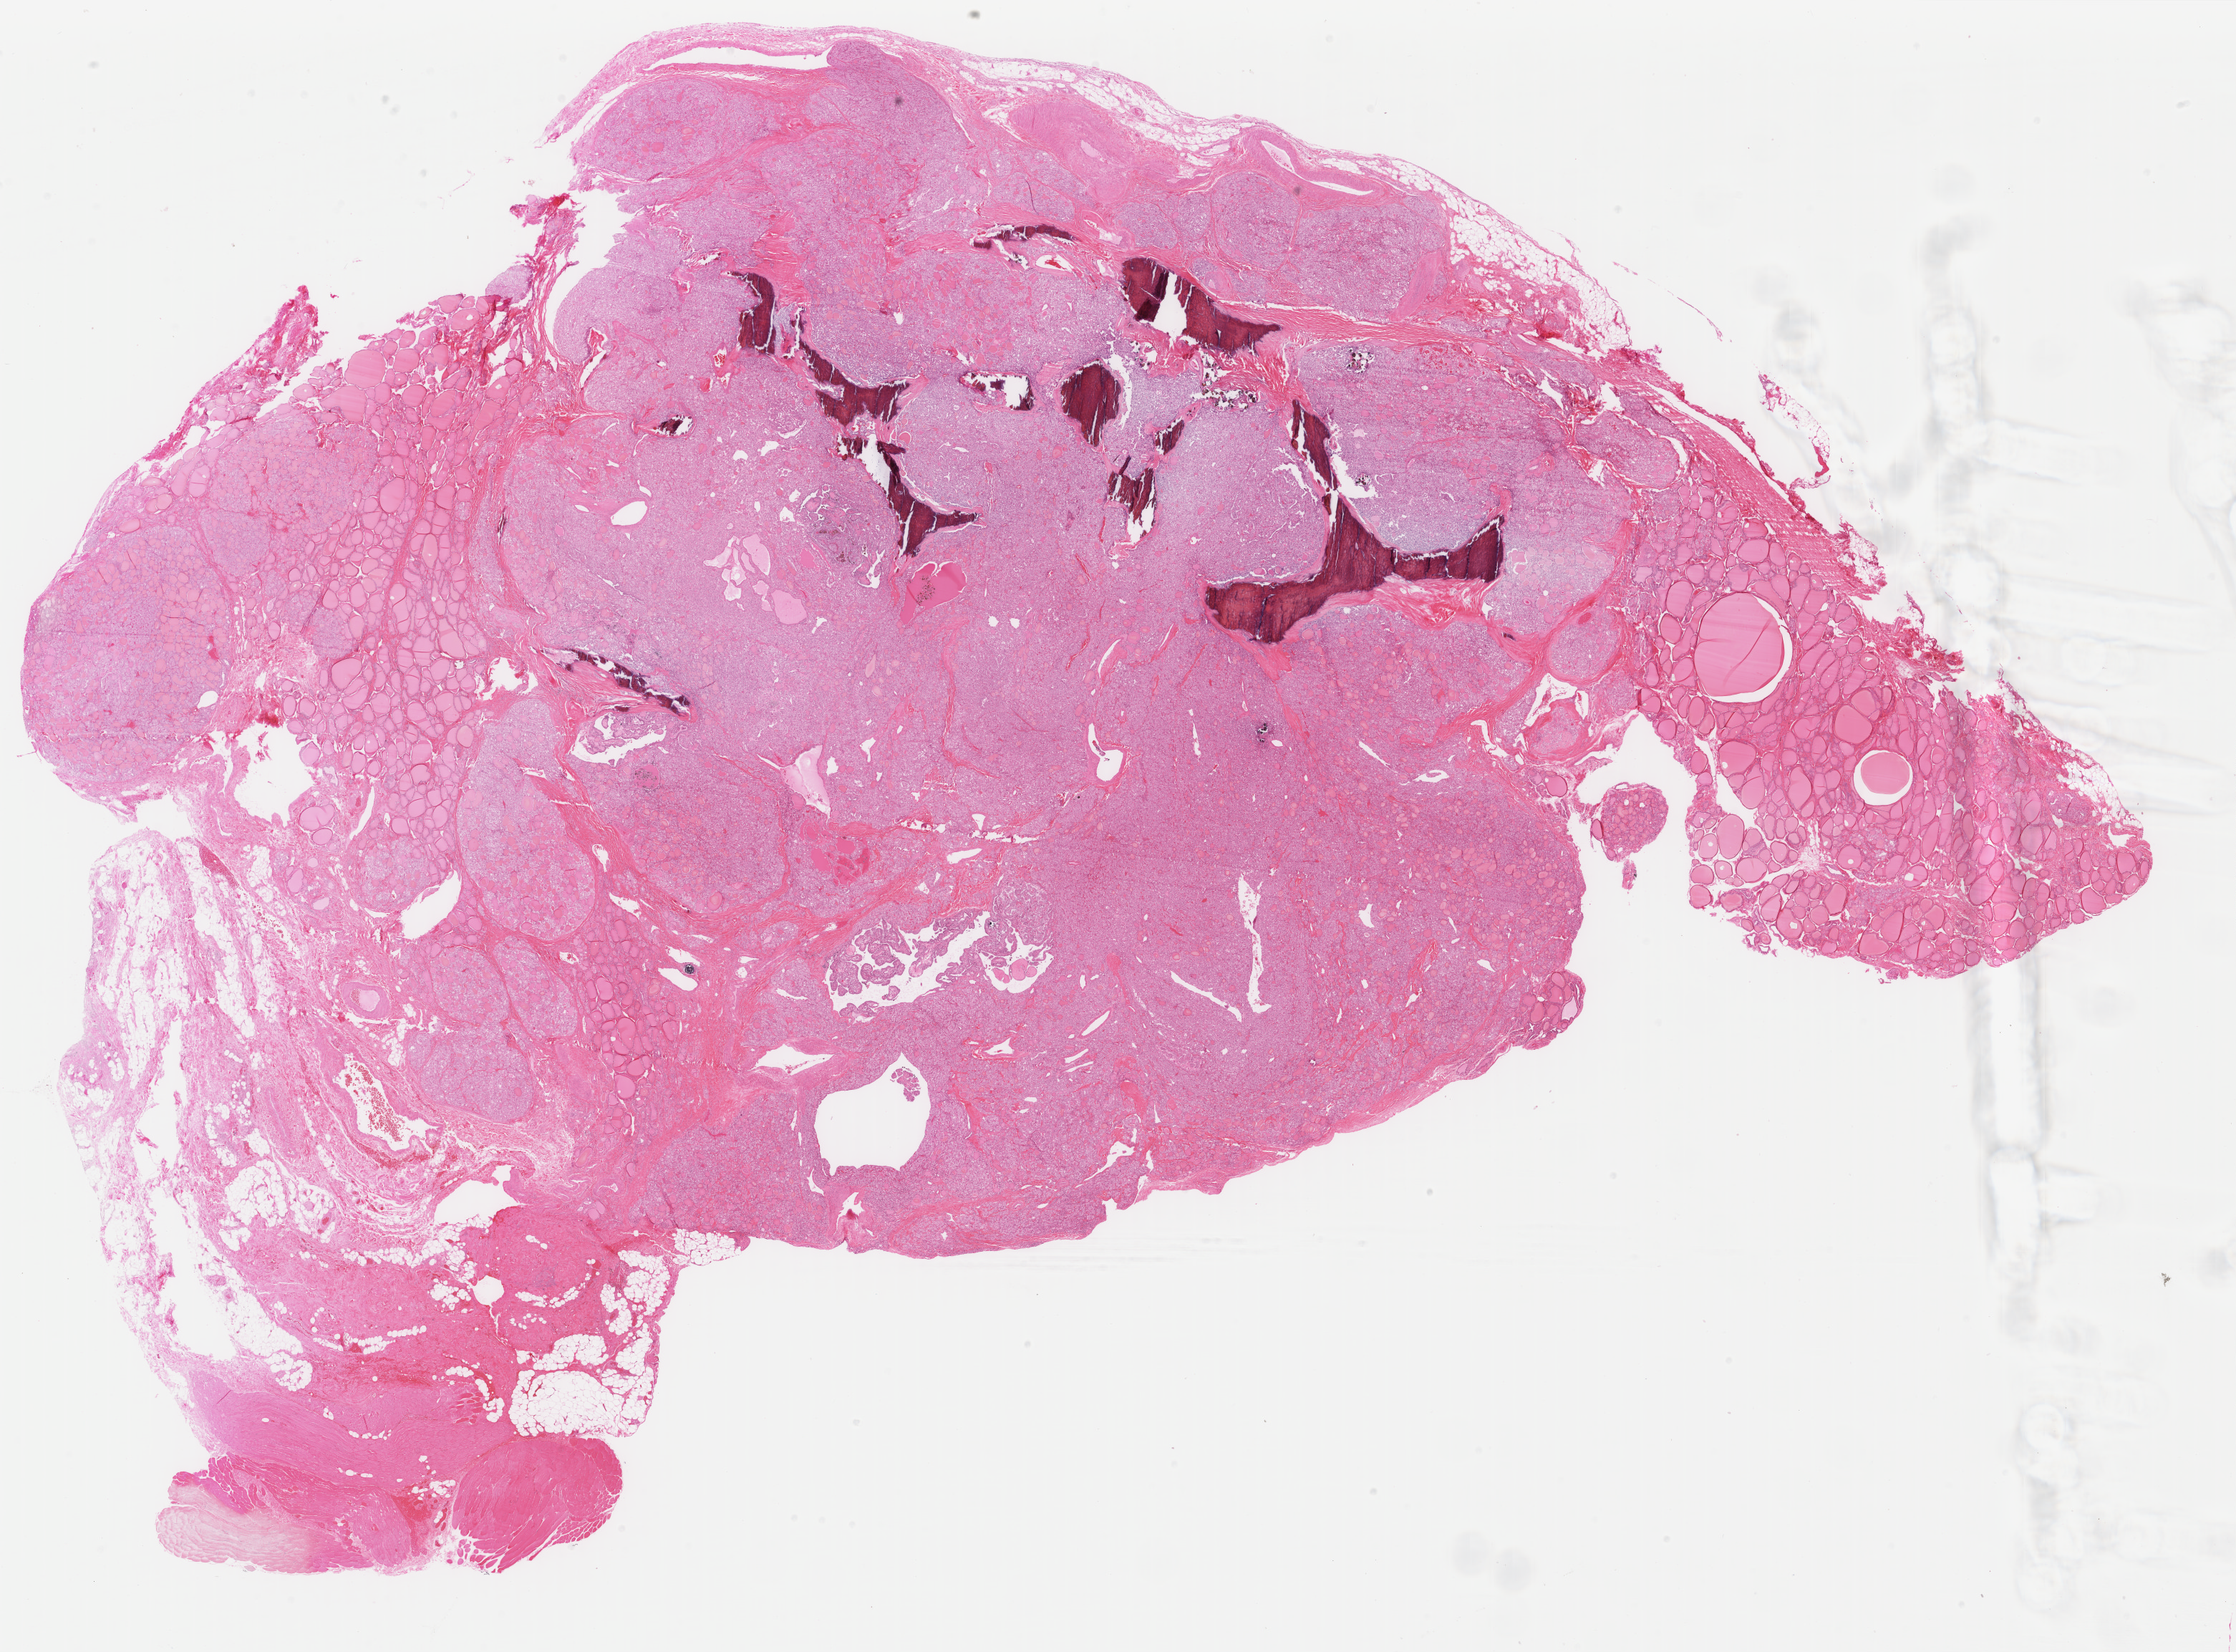
Whole-slide histology image, Hematoxylin and eosin (H&E) stained, low-resolution overview of the scanned area, about 24.8 x 18.3 mm; formalin-fixed paraffin-embedded (FFPE) diagnostic section; thyroid, primary tumour sample. Male patient; age at initial diagnosis 62 years.
Diagnosis: Papillary adenocarcinoma, NOS (thyroid gland).